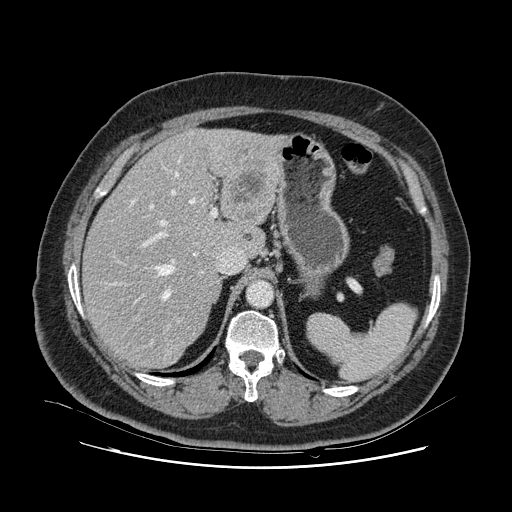
Contrast-enhanced abdominal CT, one axial slice; intravenous contrast given; soft-tissue window (W 400 / L 40 HU); 2.5 mm slice thickness; 512 × 512 image matrix. Female patient, age 73 years. From the clinical record (not read from this slice): diagnosis: colorectal cancer liver metastases, imaged before liver resection; multiple liver metastases: no; largest metastasis: 7 cm.
Annotated regions visible in this slice (outlined manually by an expert reader):
- hepatic veins: bounding box (x1, y1, x2, y2) in pixels: (131, 155, 197, 359)
- liver: (84, 129, 276, 368)
- planned liver remnant (the part of the liver to remain after resection): (84, 159, 238, 368)
- portal vein (with intrahepatic branches): (142, 204, 217, 328)
- liver metastasis: (244, 234, 252, 241)
- liver metastasis: (233, 148, 266, 218)